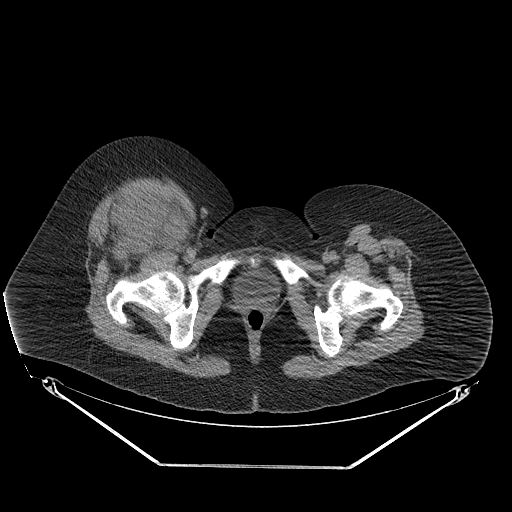
CT of an extremity soft-tissue mass (from a PET/CT study), one axial slice; slice 63 of 267 in the series (ordered by position); reconstruction kernel STANDARD; soft-tissue window (W 400 / L 40 HU); 3.75 mm slice thickness; 512 × 512 image matrix. Female patient. From the clinical record (not read from this slice): histological type: malignant solitary fibrous tumor; grade: intermediate; site of the primary tumour: right thigh.
Outlined on this slice (expert contour drawn on MRI and transferred to this co-registered scan by the dataset authors):
- gross tumour volume including surrounding oedema: bounding box <103,190,174,243> (left, top, right, bottom; pixels)
- gross tumour volume (mass): <125,194,158,225>